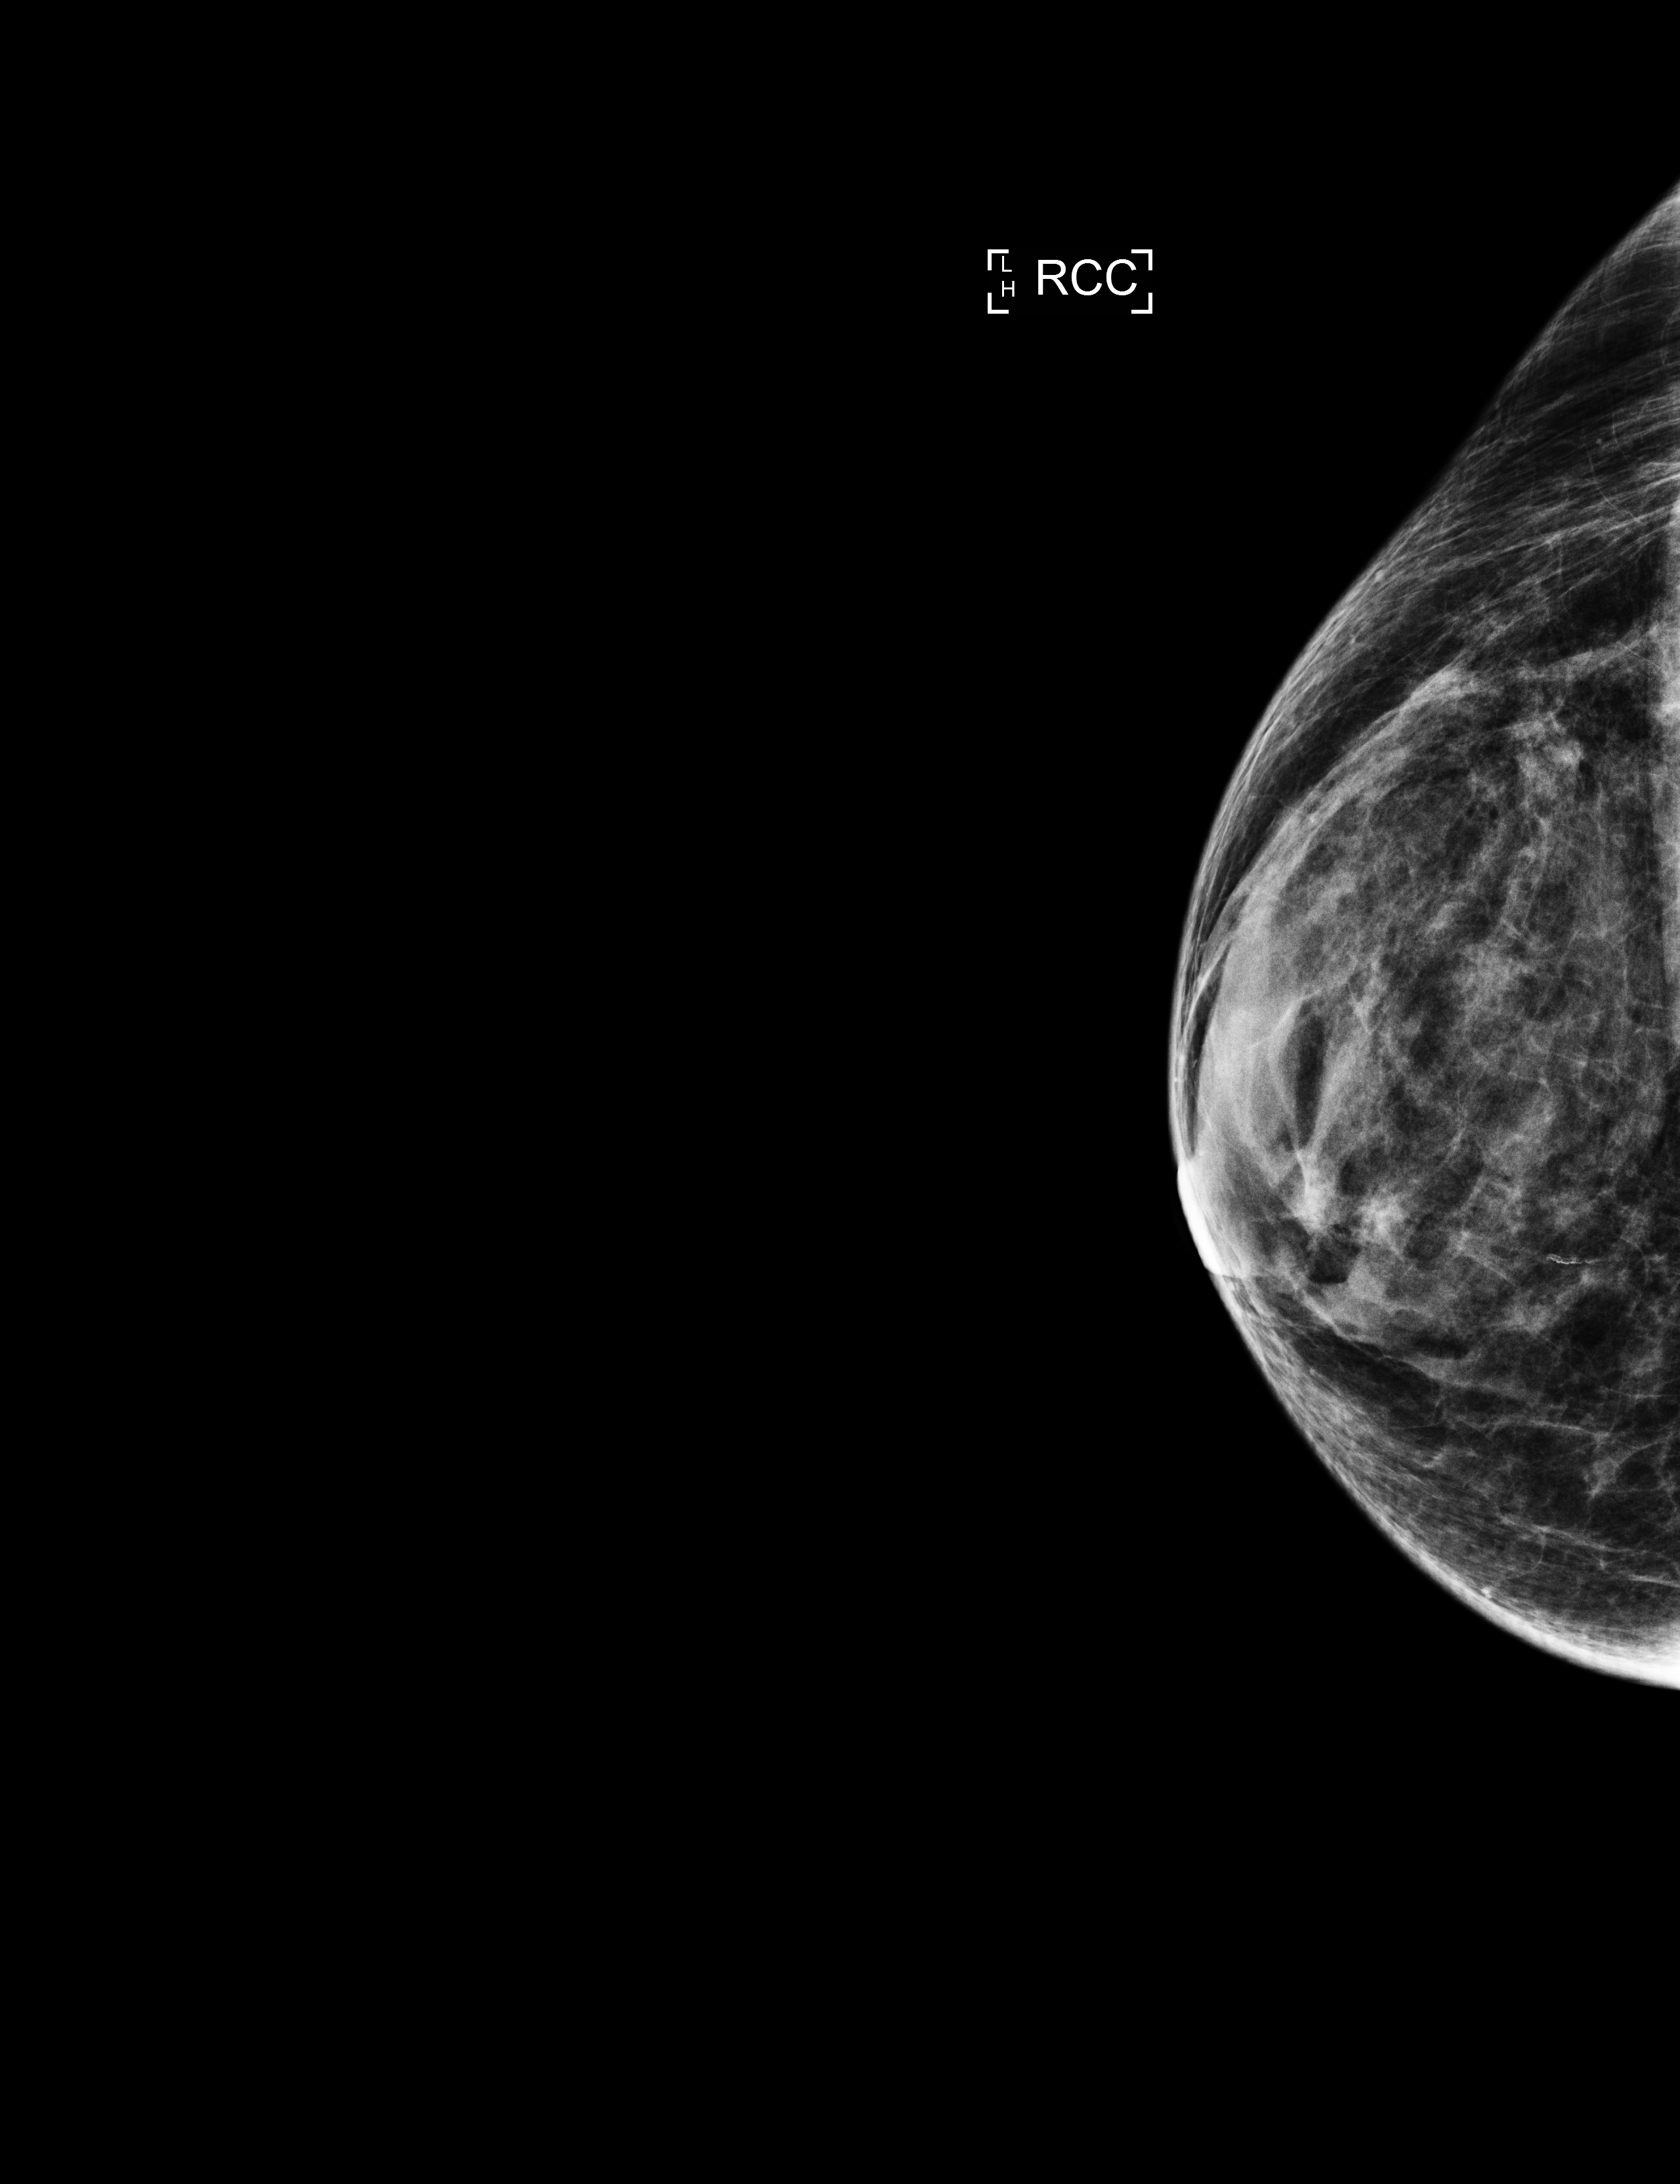
Annual screening mammography examination, compressed breast thickness 33 mm, system: Selenia Dimensions. Female patient, age 67 years.
Image type: full-field digital mammogram. Breast: right. Projection: cranio-caudal projection.